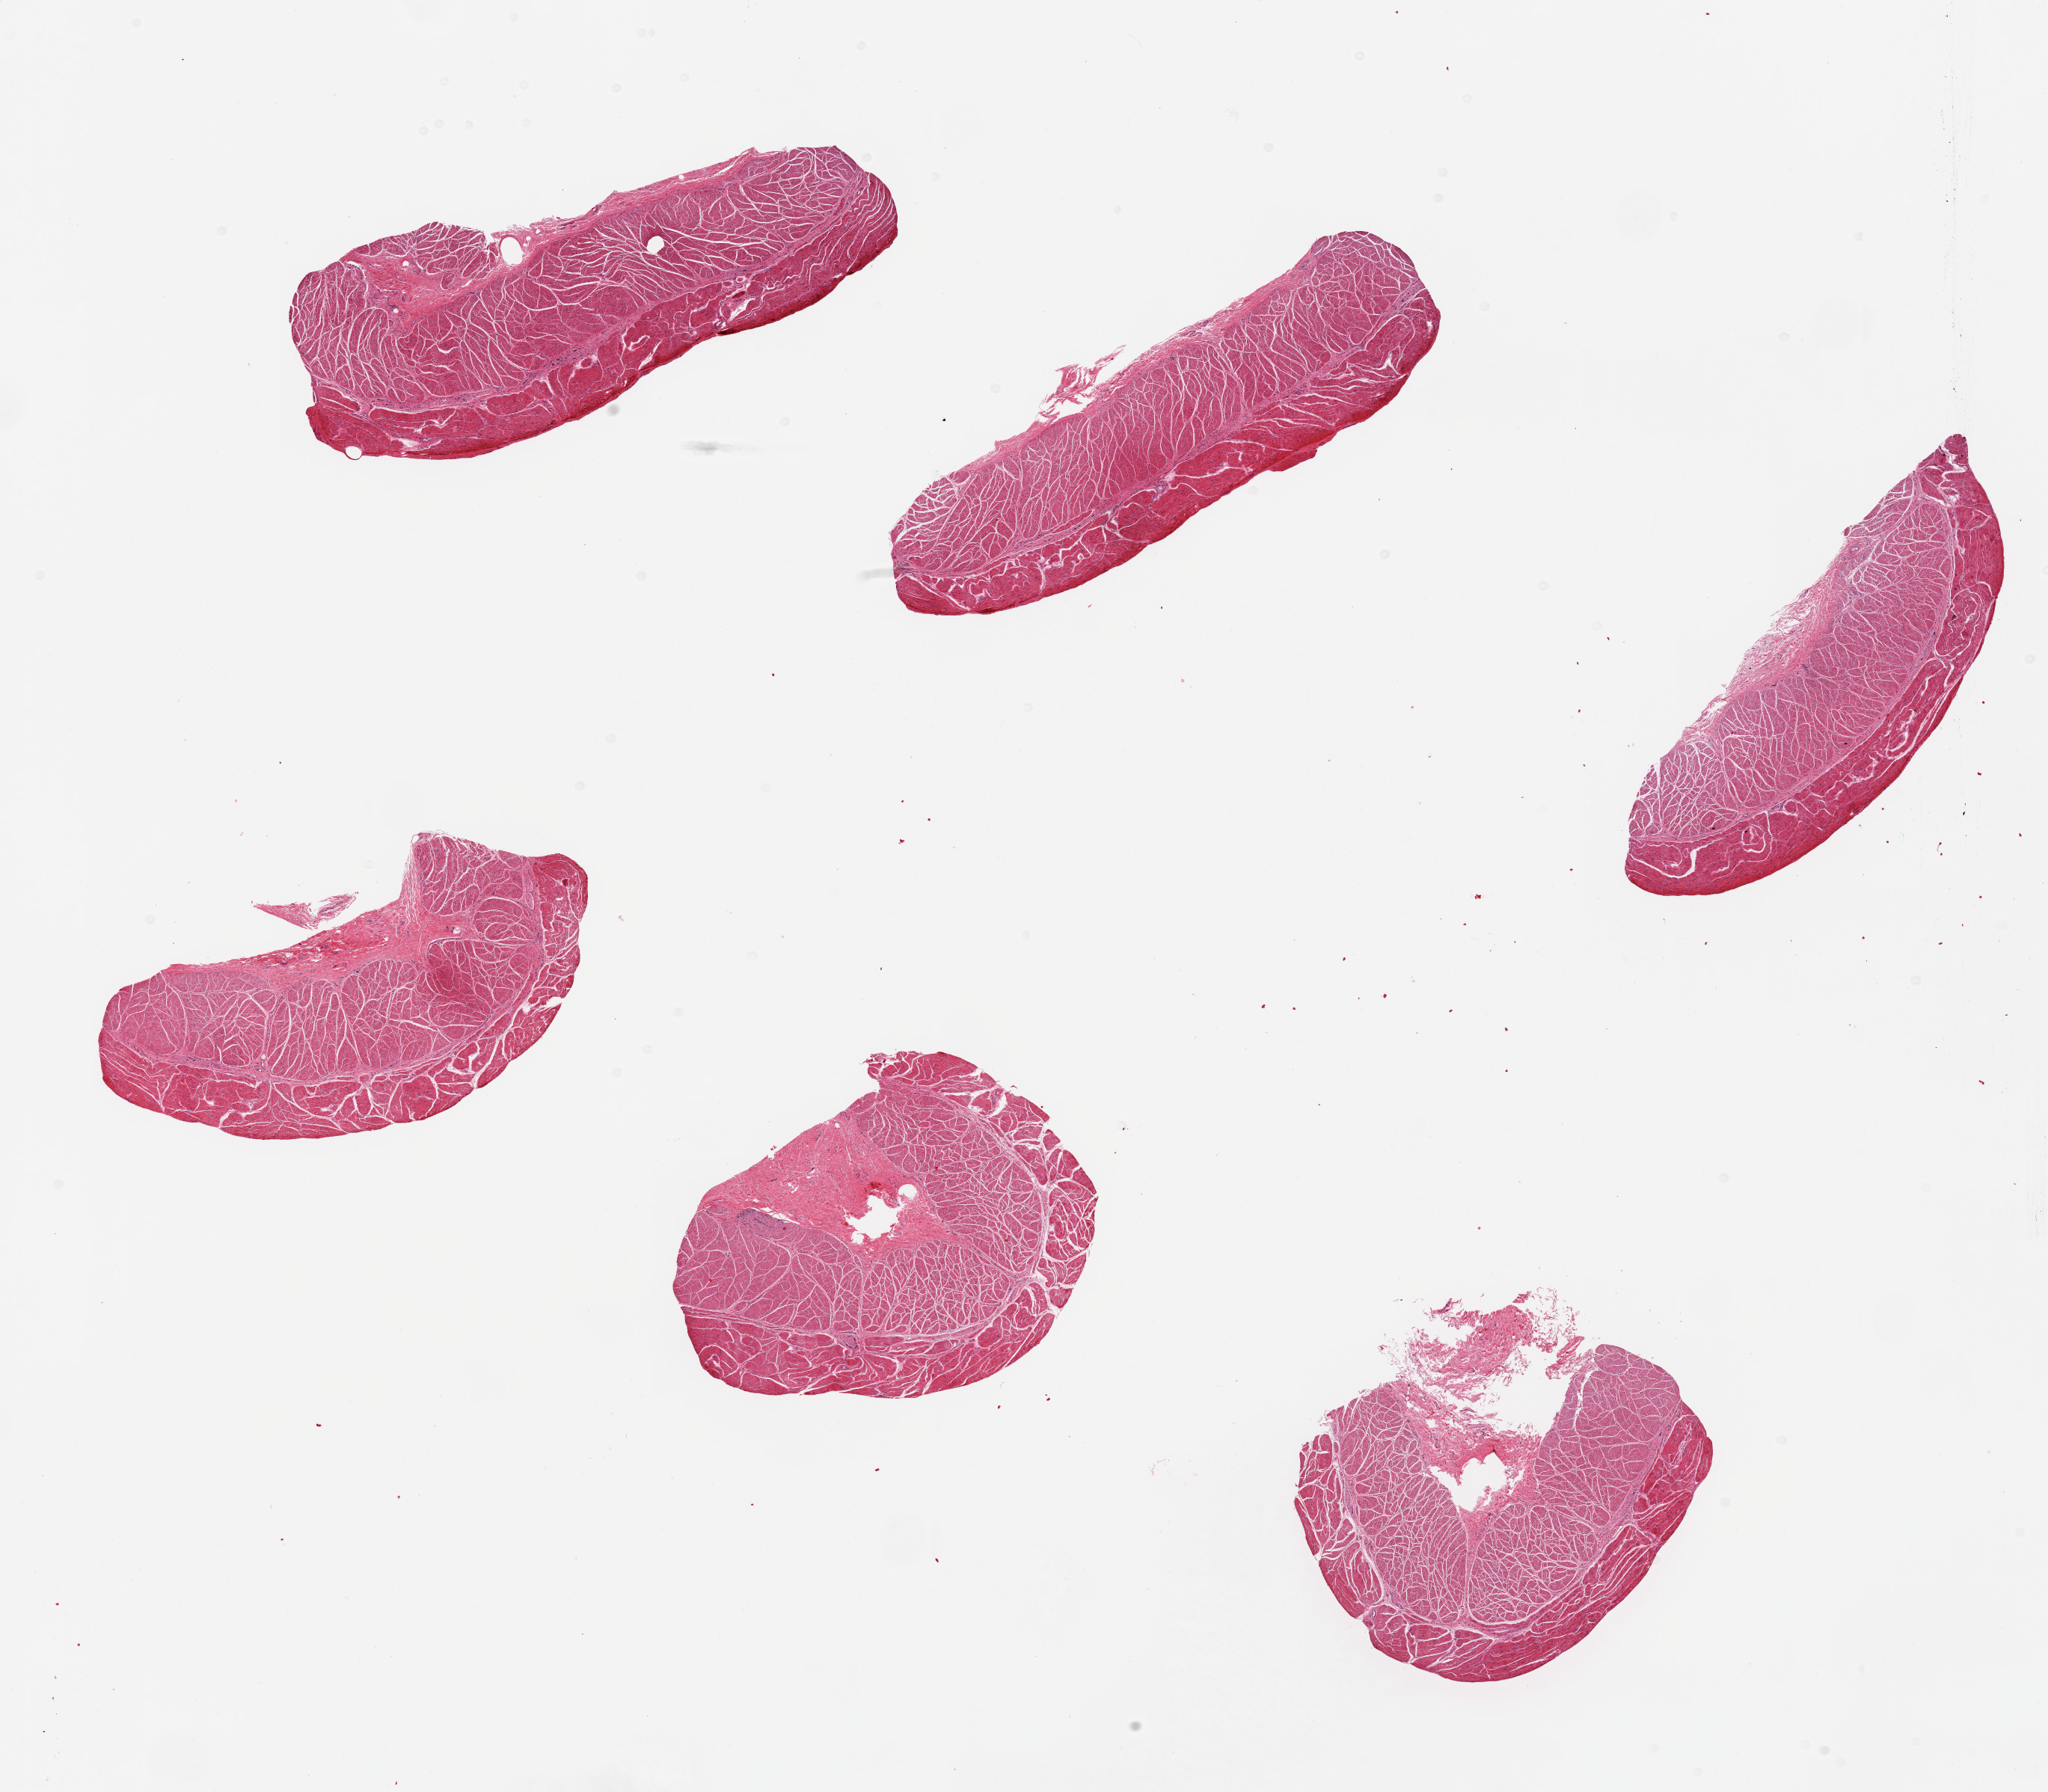
Whole-slide image, haematoxylin and eosin stain, shown as a low-resolution overview of the whole scanned area (about 21.7 x 19.0 mm). PAXgene-fixed paraffin-embedded (PFPE) section. Sampled site (target tissue): esophageal muscle. Tissue donor sample. Donor: male.
• pathologist's review note for this sample: 6 pieces; well trimmed